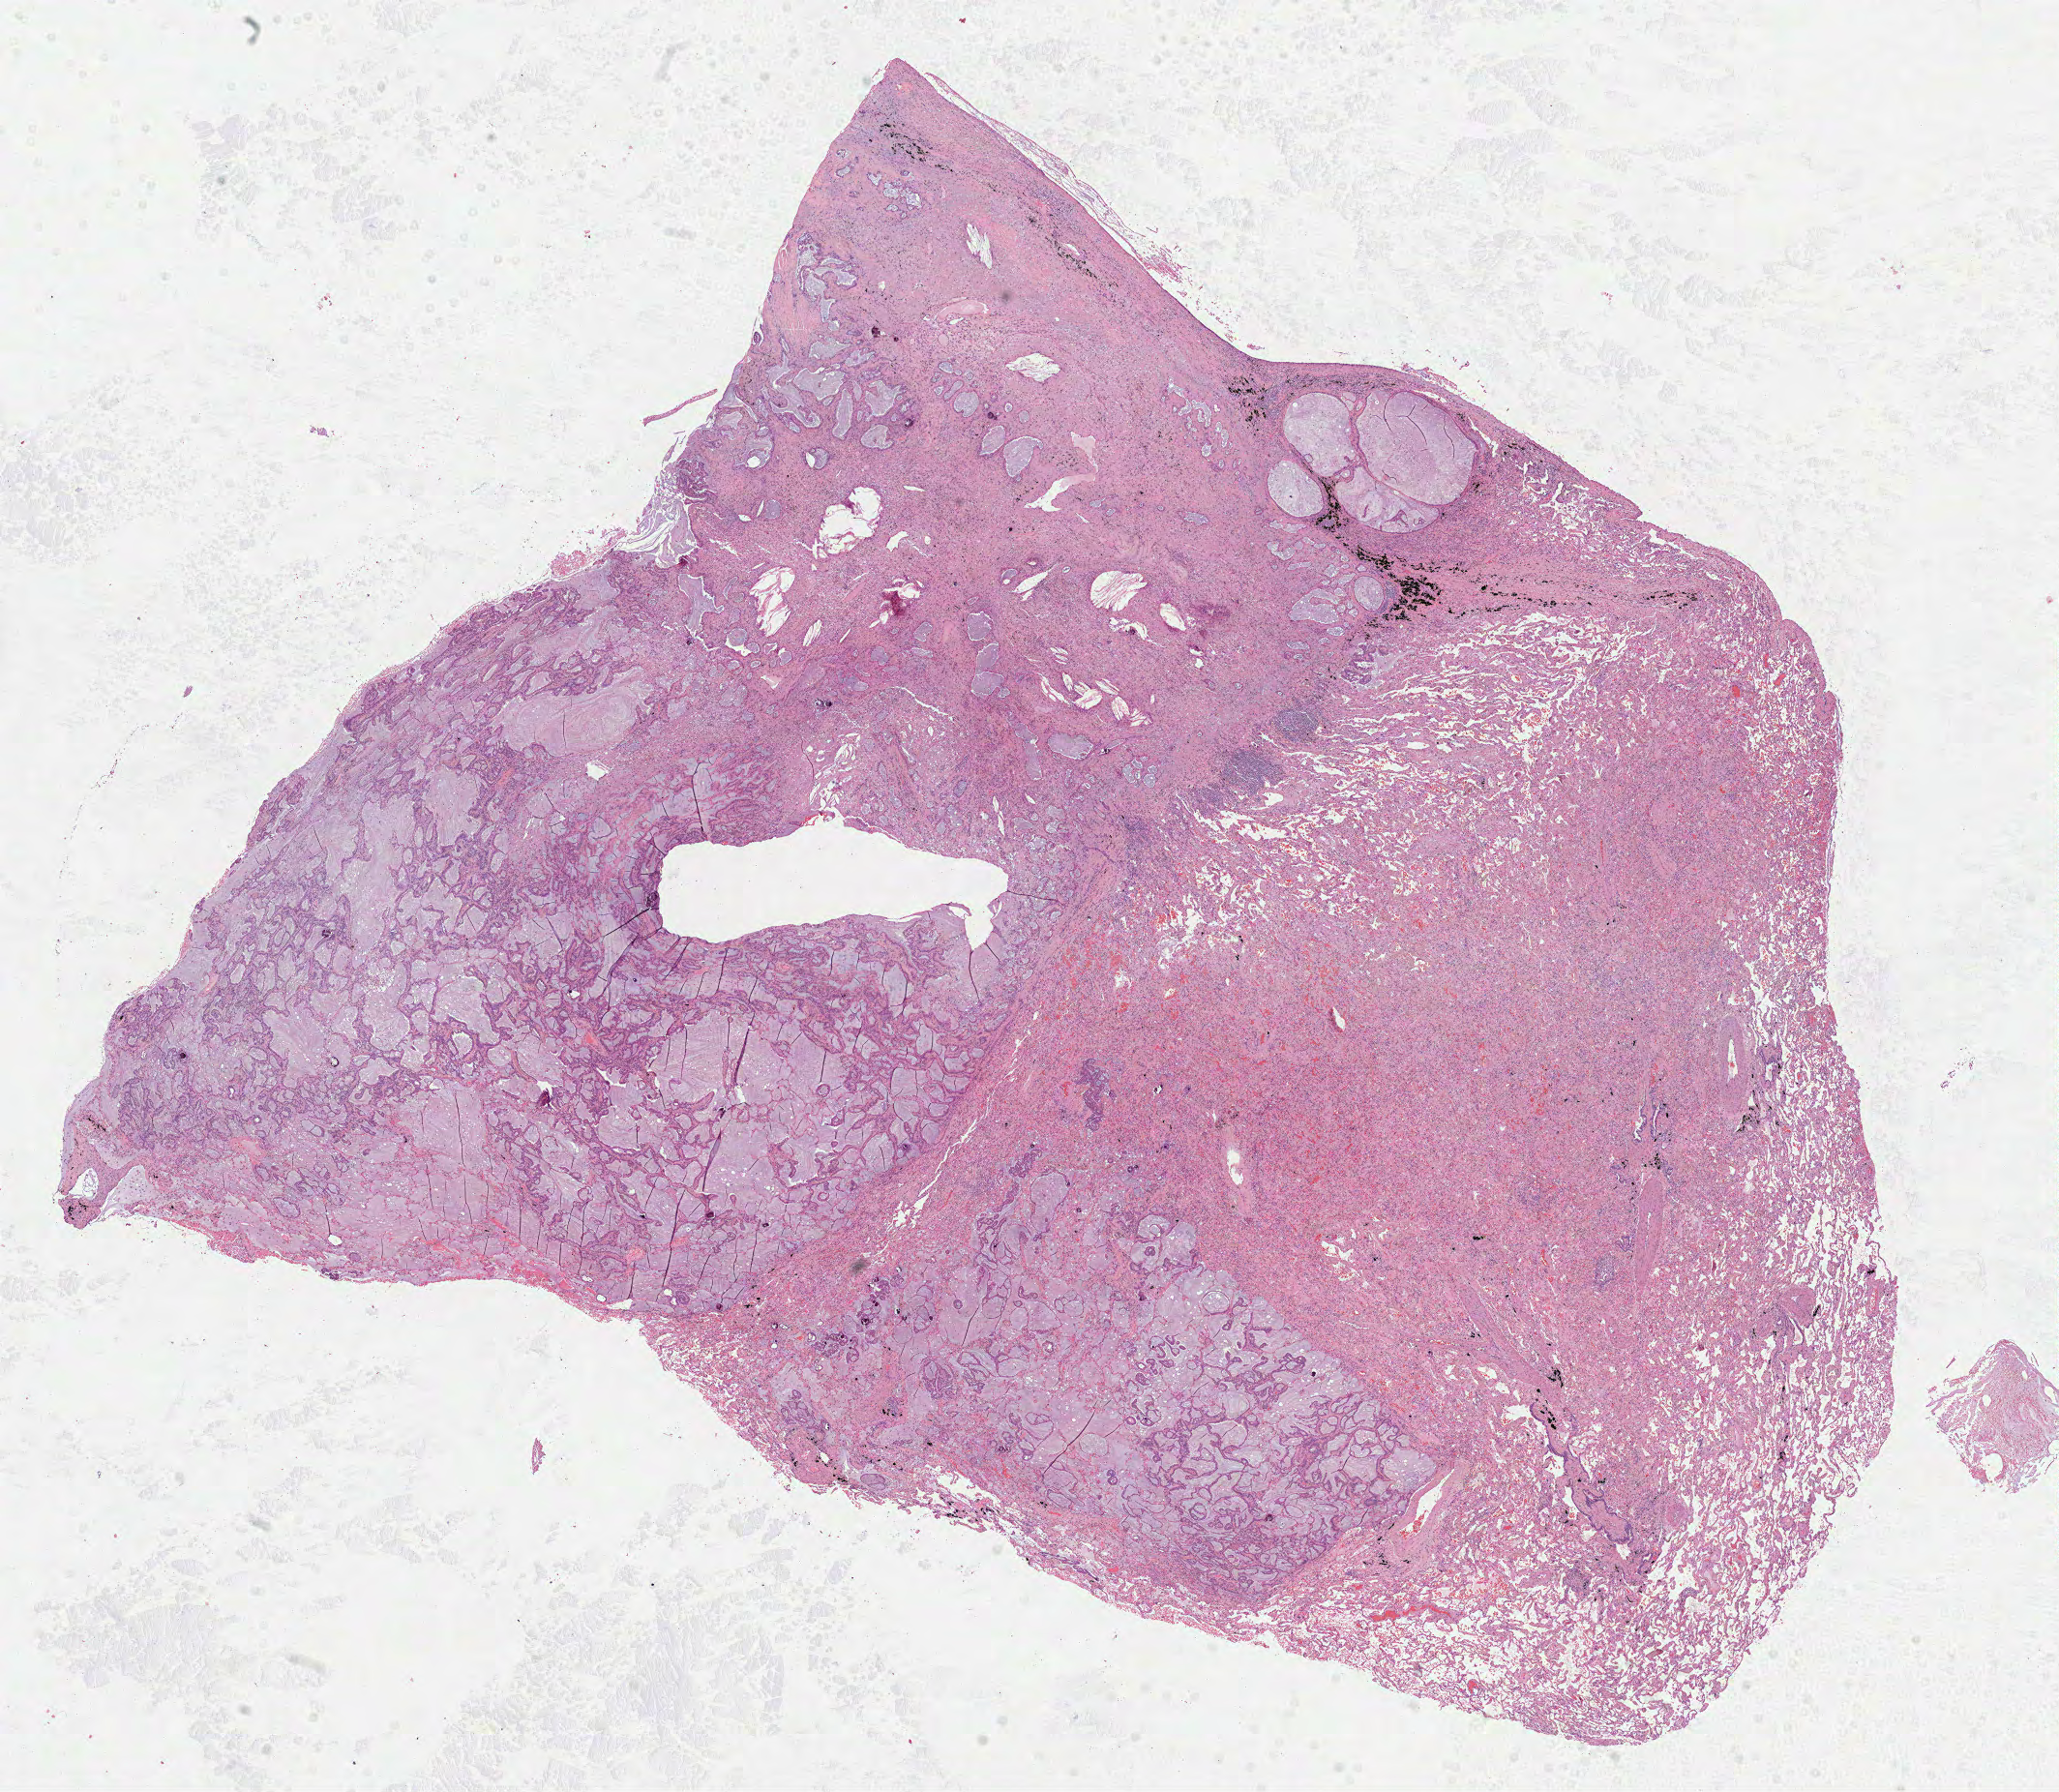
Digitized H&E tissue section (whole slide) — whole scanned area (about 17.2 x 14.9 mm, from a 40x scan) shown as a low-resolution overview; formalin-fixed paraffin-embedded (FFPE) diagnostic section; primary tumour sample from the lung. Female, age 60 years at initial diagnosis.
TNM: T1b N0 MX. AJCC pathologic stage: IA. Histologic diagnosis: Bronchio-alveolar carcinoma, mucinous.